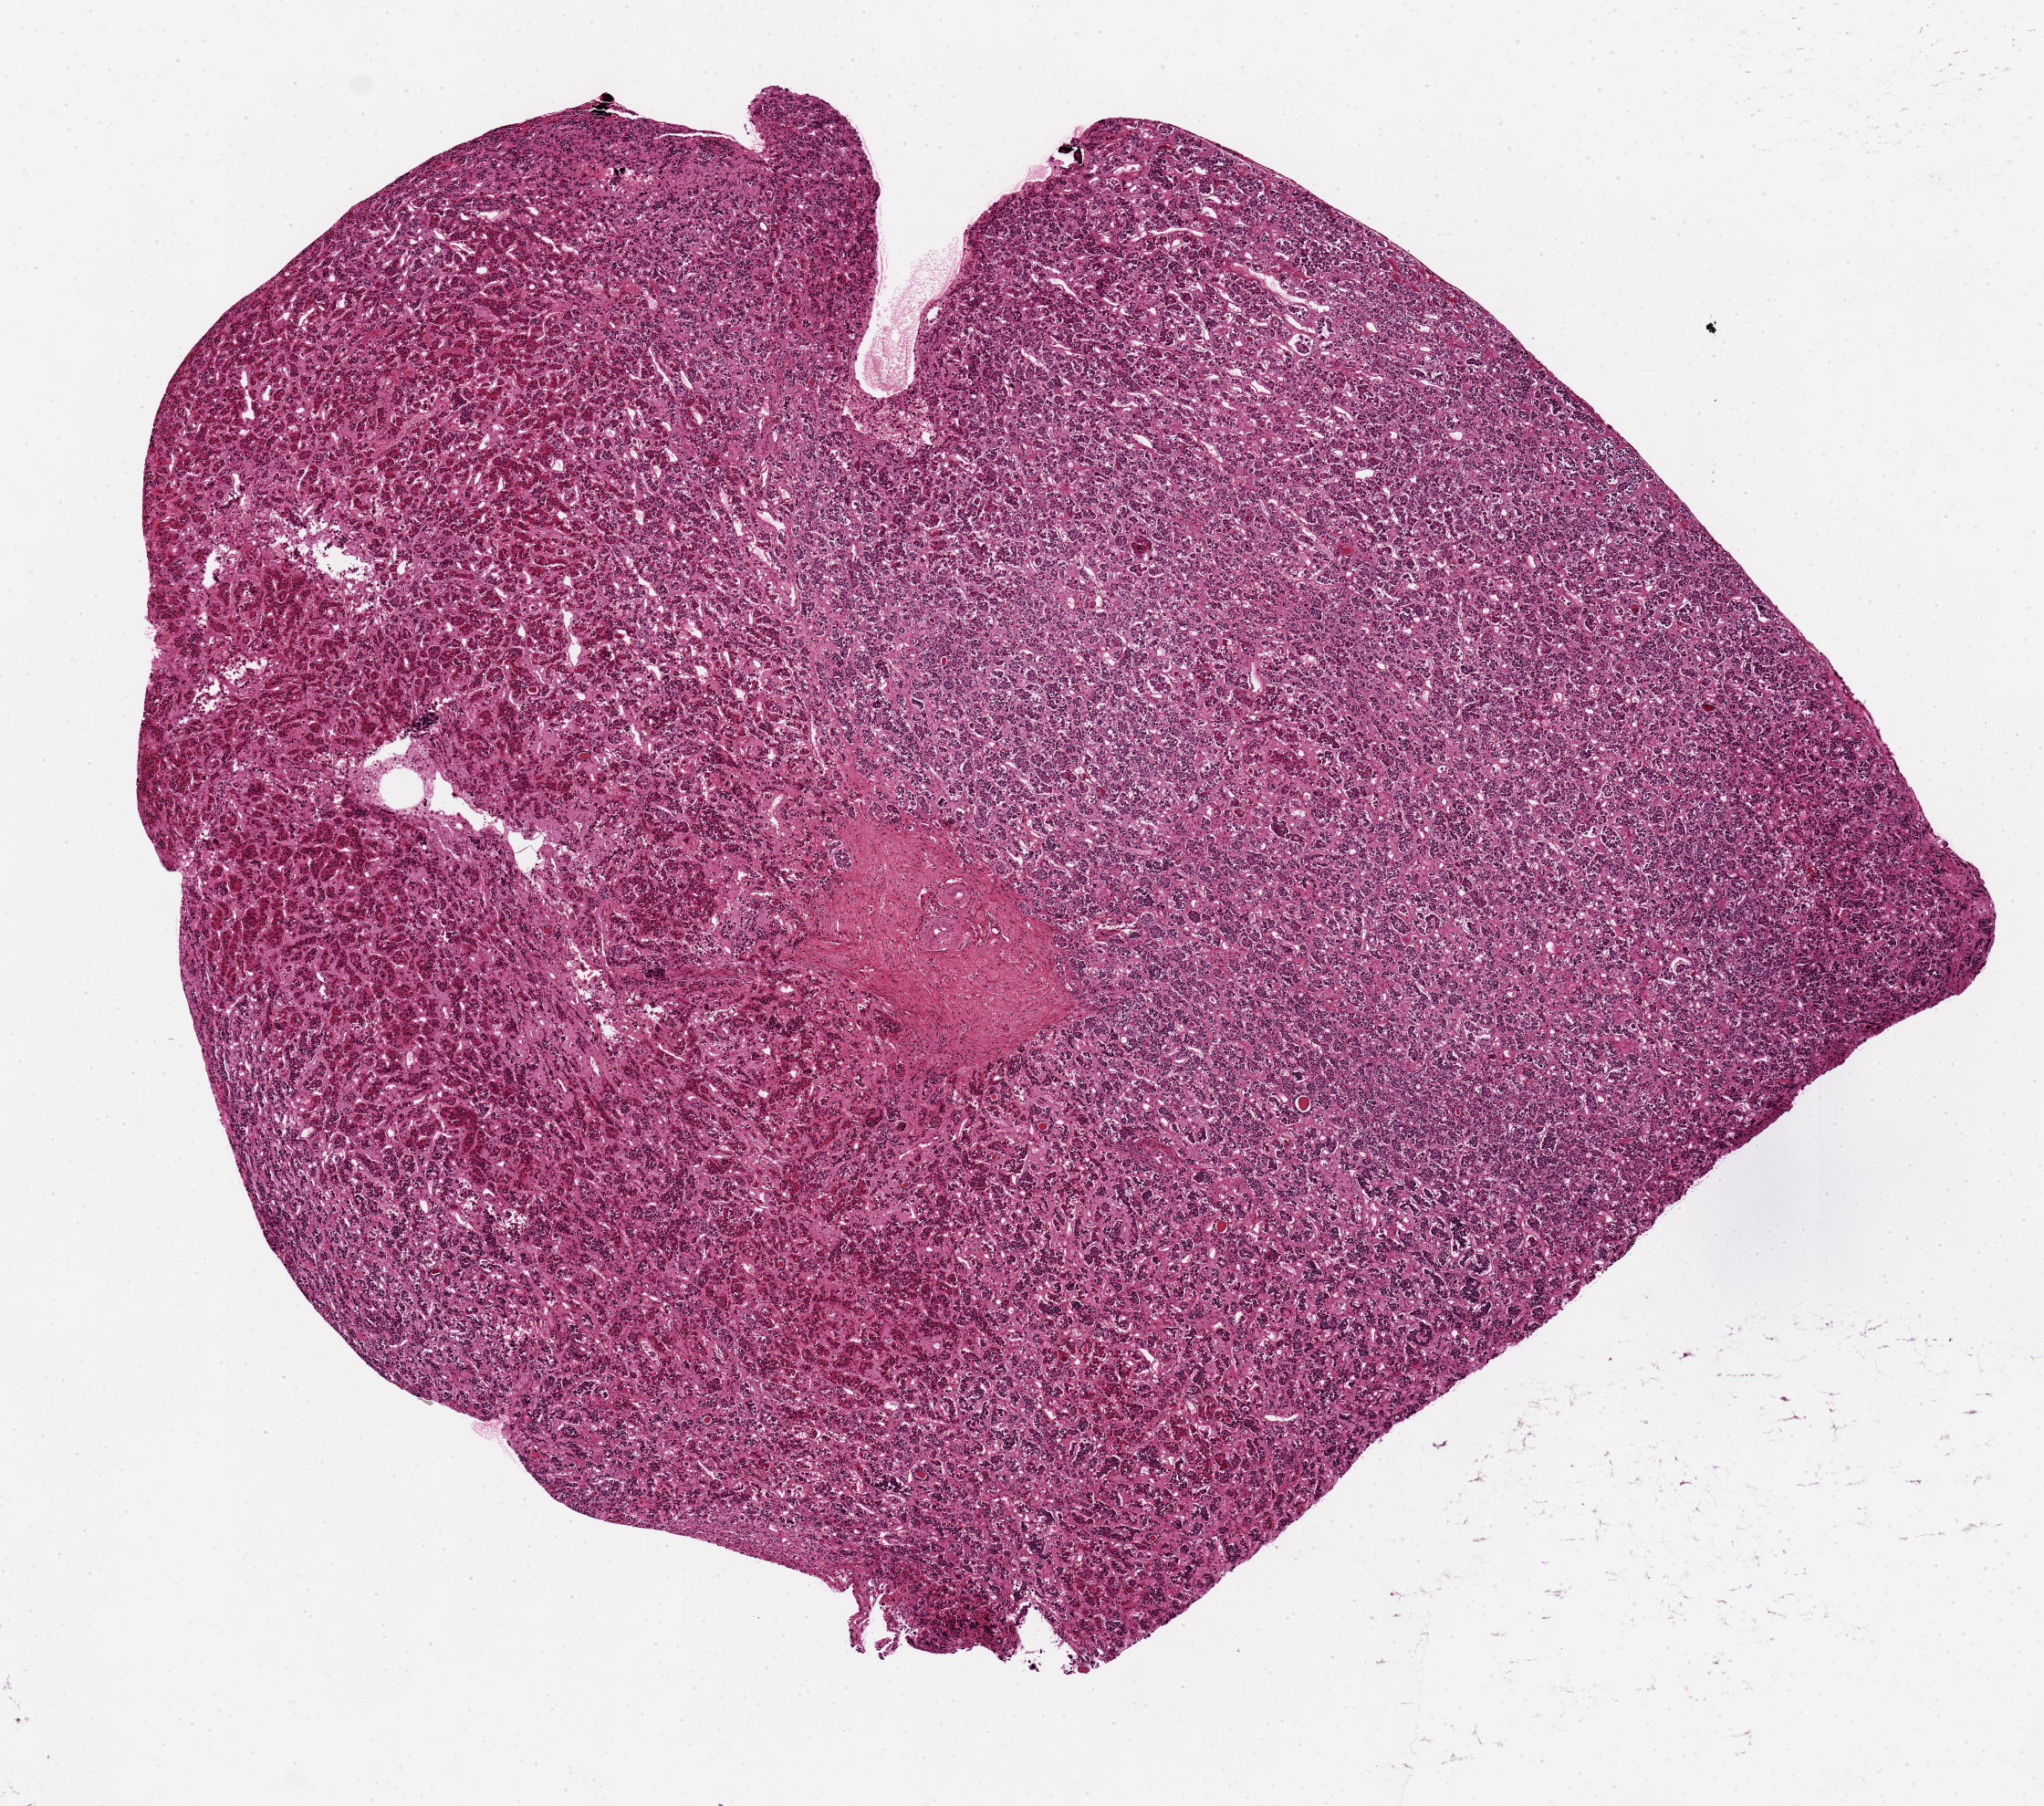
Digitized hematoxylin and eosin (H&E)-stained section, brightfield, a low-resolution overview of the entire scanned area, about 8.9 x 7.8 mm (slide scanned at 20x). PAXgene-fixed paraffin-embedded (PFPE) section. Section of pituitary (target tissue). Donor tissue sample. Donor: female.
Reviewer comment on this tissue sample: 7 x 6mm specimen.